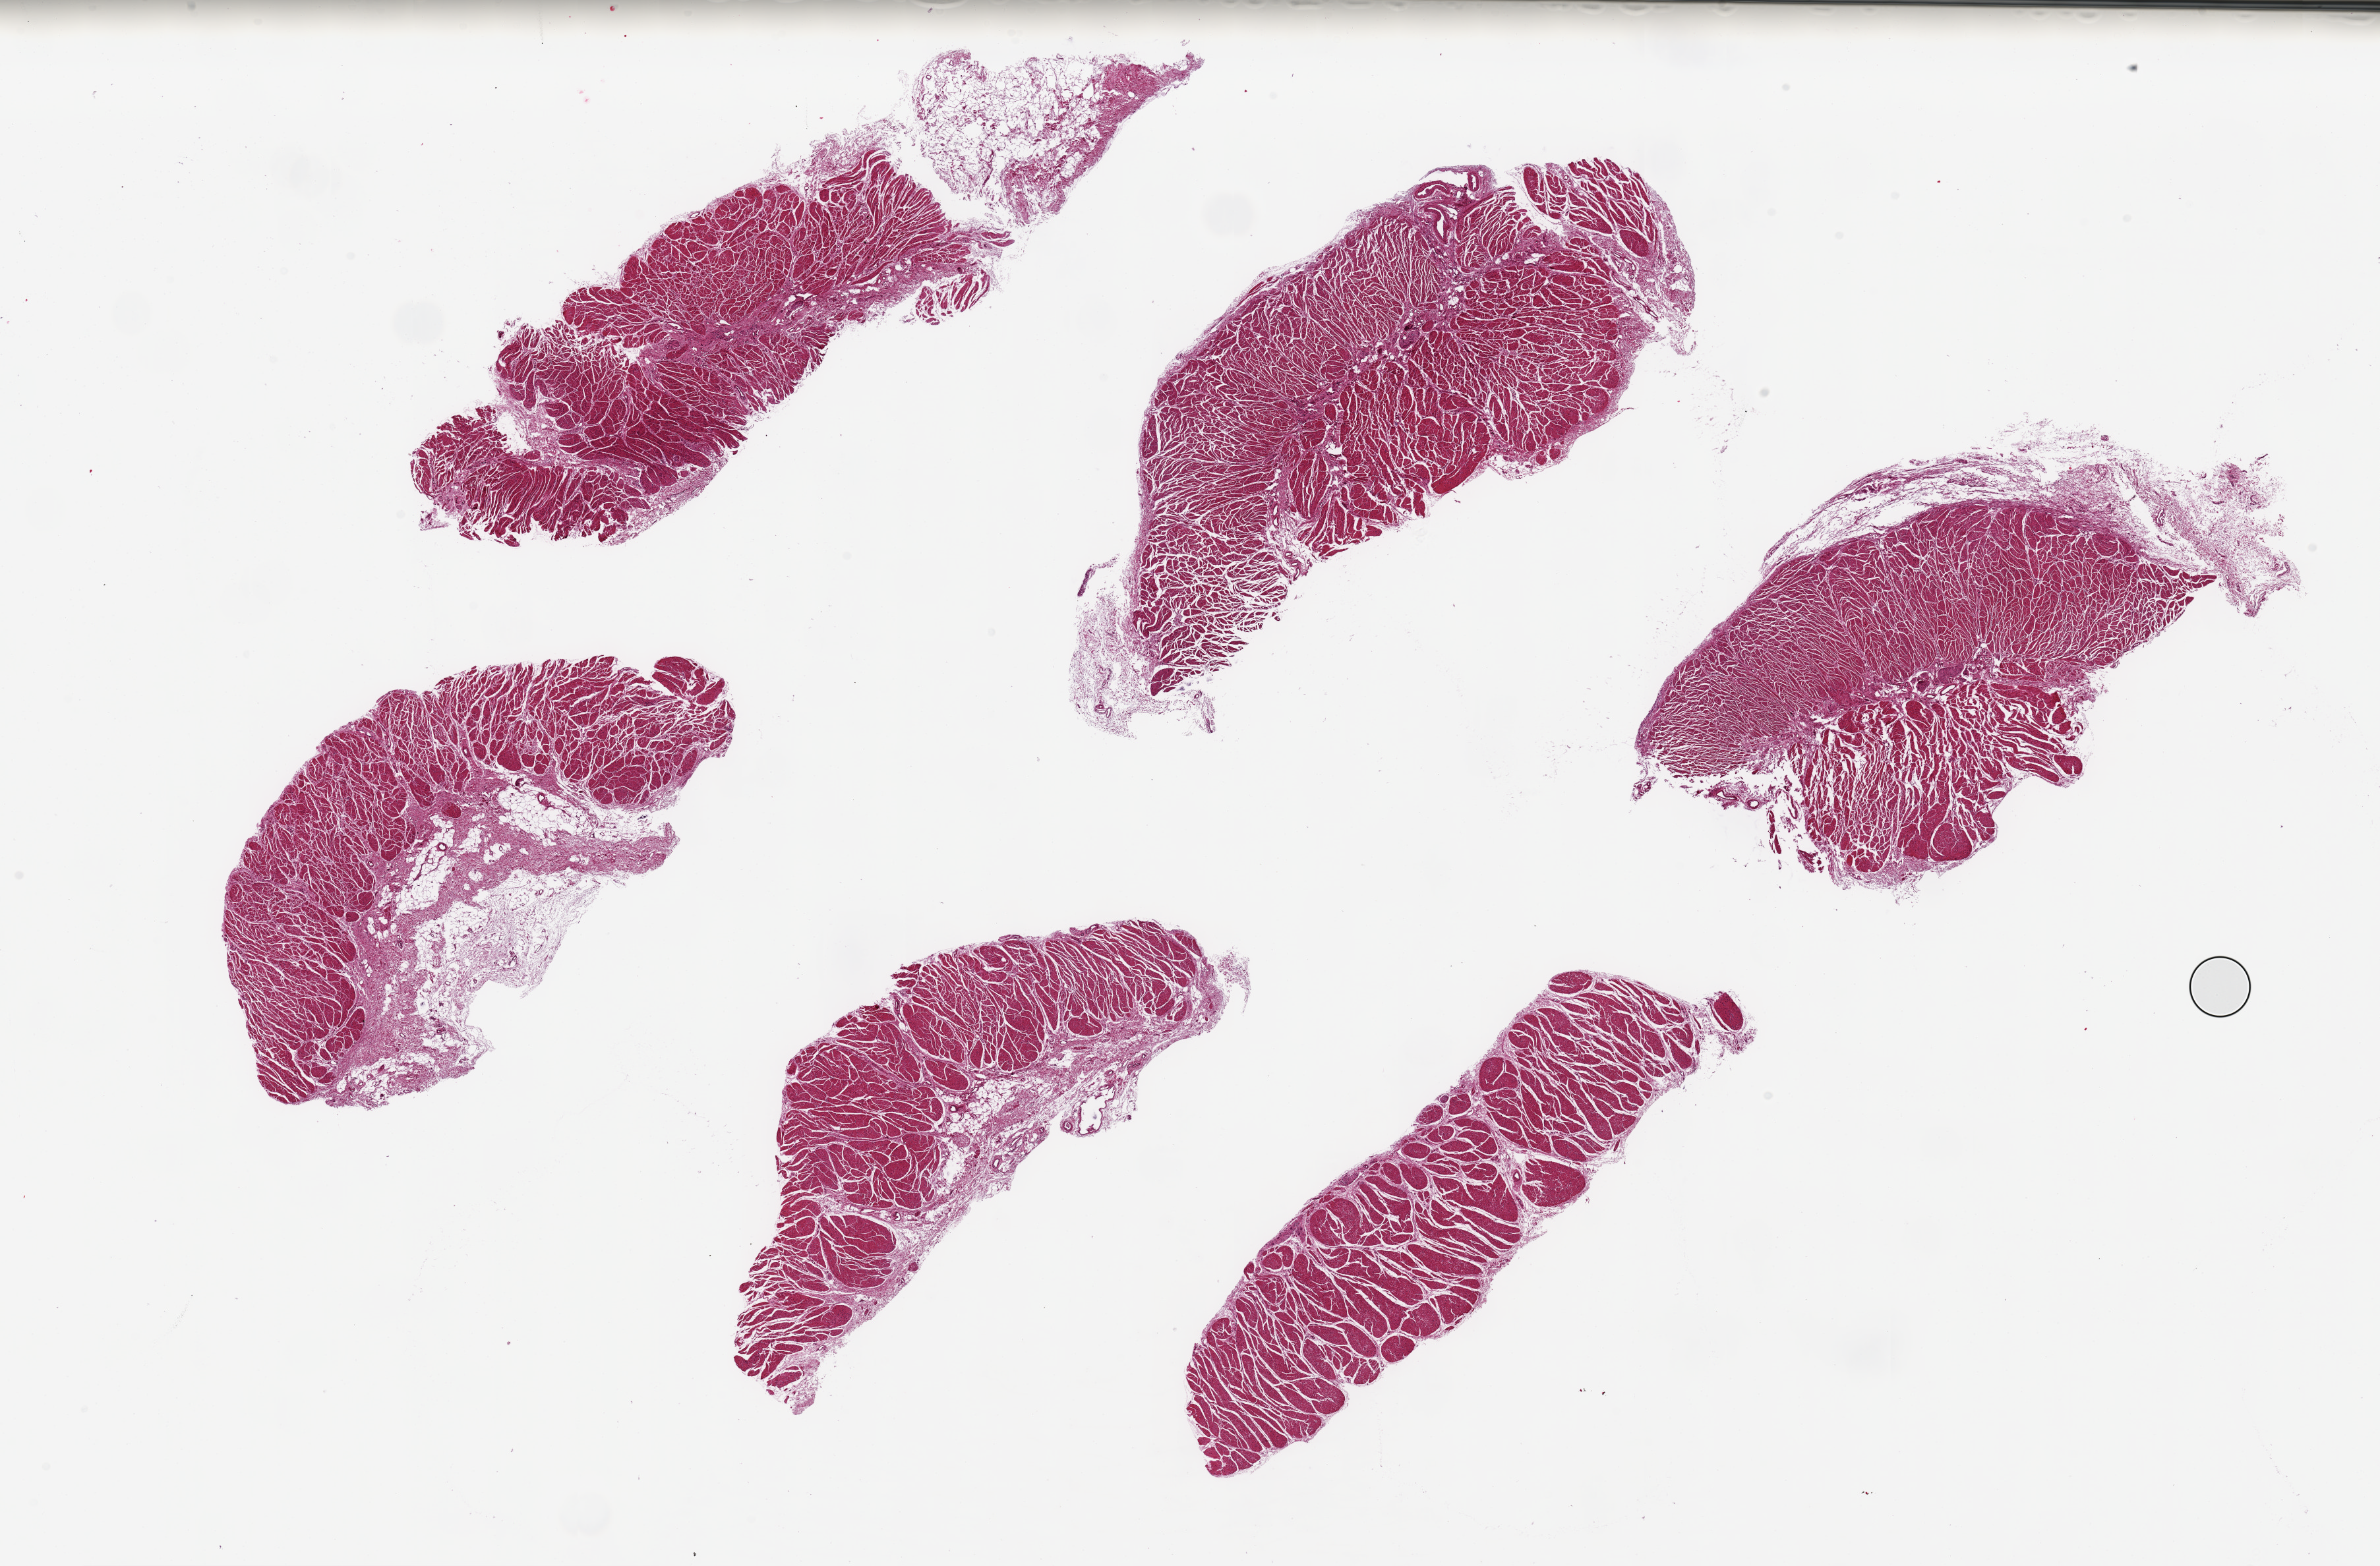
Digitized haematoxylin and eosin-stained section, brightfield — shown as a low-resolution overview of the whole scanned area (about 28.5 x 18.8 mm, slide scanned at 20x); PAXgene-fixed, paraffin-embedded tissue; sampled site (target tissue): esophageal muscle; tissue donor sample. Male donor.
Review note (as recorded): 6 ~8x2.5mm pieces.